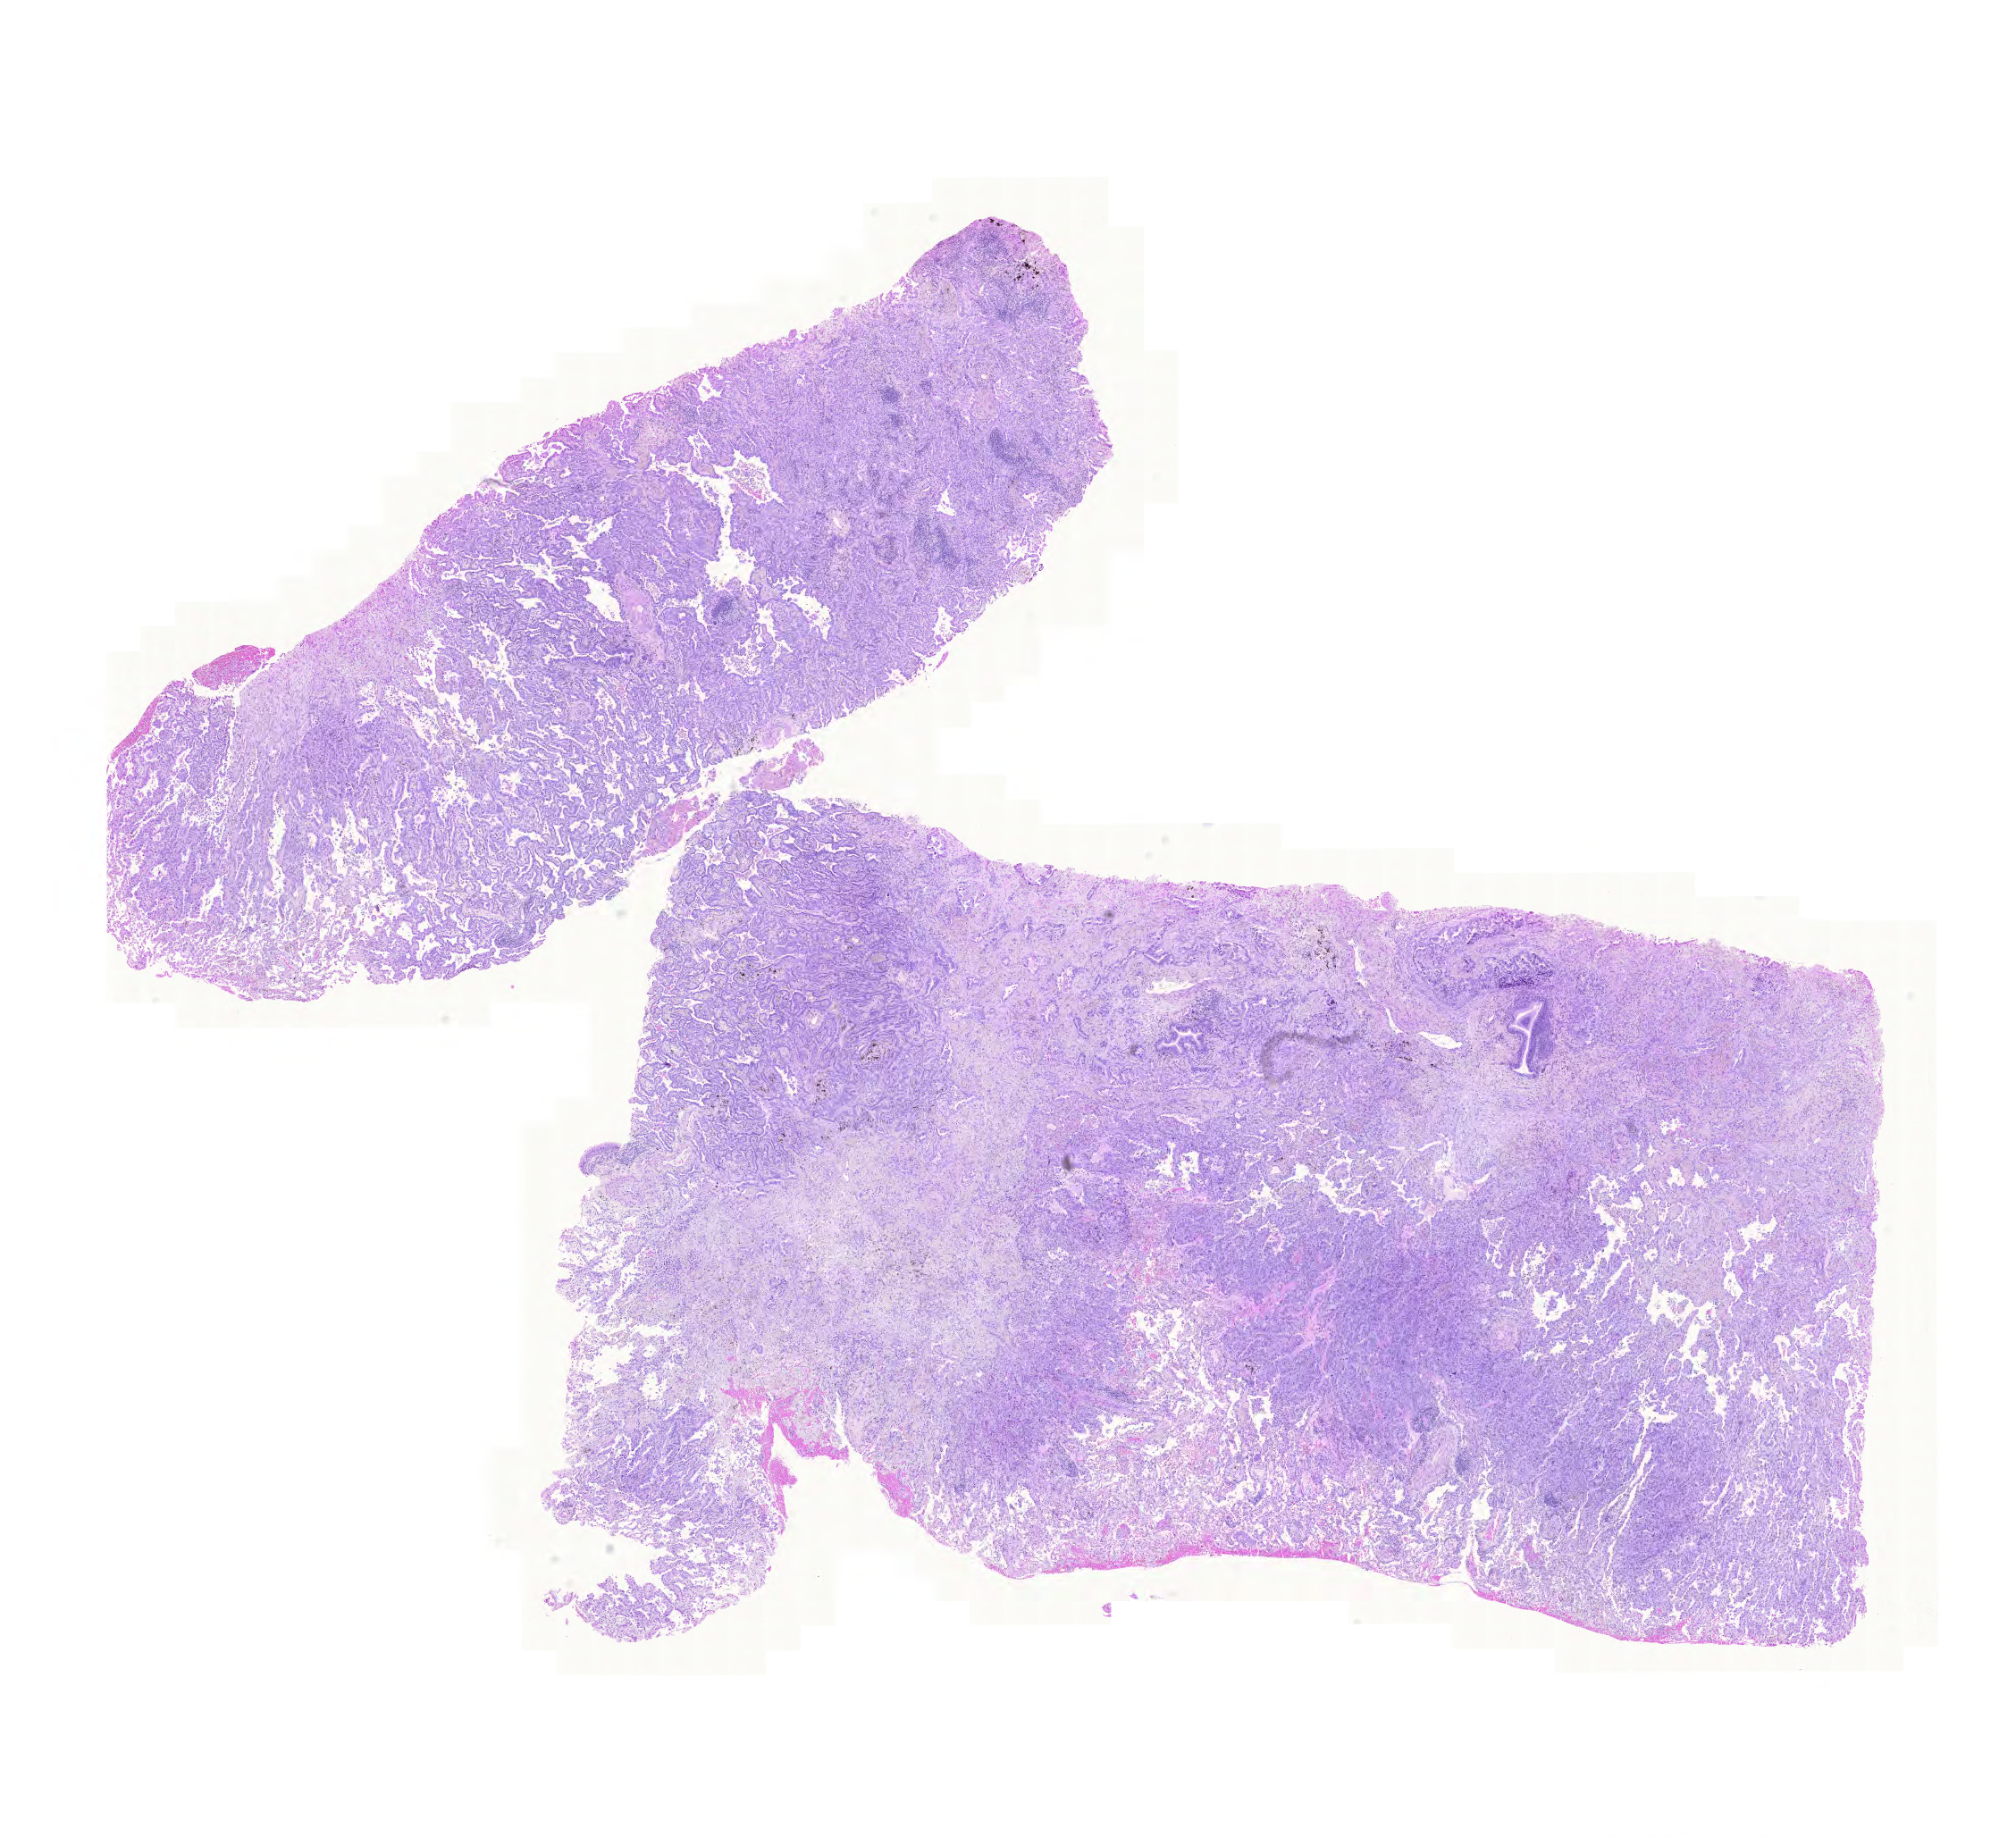
Whole-slide histology image, Hematoxylin and eosin (H&E) stained — low-resolution overview of the scanned area, about 16.8 x 15.3 mm (acquisition: 20x scan). FFPE section. Lung, primary tumour sample. Female patient; age at initial diagnosis 59 years.
Diagnosis: Adenocarcinoma with mixed subtypes (lower lobe, lung).